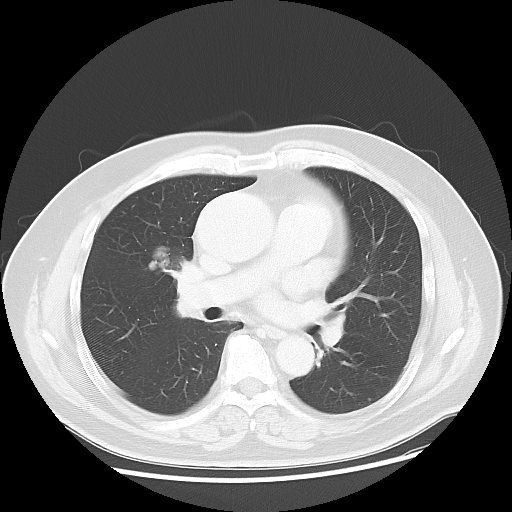
Chest CT, one axial slice. Position 23 of 48 along the scan axis. Reconstruction kernel LUNG. 120 kVp. Lung window (W 1500 / L -600 HU). 5 mm slice thickness. 512 × 512 image matrix, field of view 392 × 392 mm. Male patient, age 60 years. Case-level facts recorded for this patient, not image findings: clinical TNM (as recorded): T2 N3 M0.
Outlined on this slice (bounding box drawn by a radiologist):
- lung tumour (recorded histology: adenocarcinoma): bounding box [x1, y1, x2, y2] px = [143, 236, 195, 282]